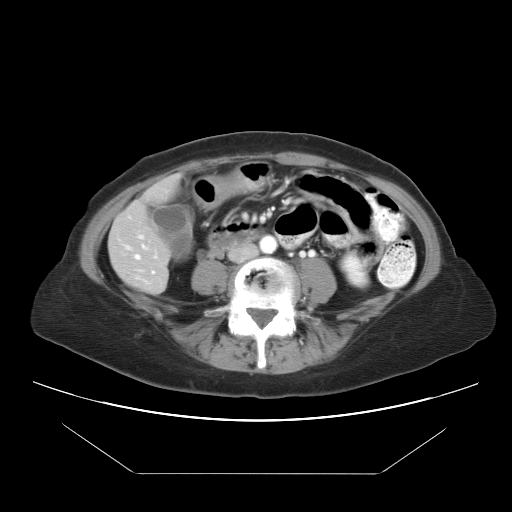
Contrast-enhanced abdominal CT, one axial slice. Slice 2 of 21 in the series (ordered by position). Reconstruction kernel STANDARD. 120 kVp. Intravenous contrast given. Soft-tissue window (W 400 / L 40 HU). 512 × 512 image matrix, field of view 392 × 392 mm. Female patient, age 72 years. From the clinical record (not read from this slice): diagnosis: colorectal cancer liver metastases, imaged before liver resection; multiple liver metastases: yes.
Outlined on this slice (expert manual segmentation):
- hepatic veins: box from (x=136, y=246) to (x=145, y=258) px
- liver: (x=110, y=183)–(x=174, y=293)
- planned liver remnant (the part of the liver to remain after resection): (x=110, y=184)–(x=173, y=293)